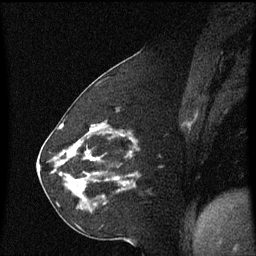
Breast MRI (dynamic contrast-enhanced), one sagittal slice; slice 23 of 60 in the series (ordered by position); dynamic contrast-enhanced series, image 2 of 3 at this slice position (ordered by acquisition); 1.5 T; TE 4.2 ms, TR 8.4 ms; 2.2 mm slice thickness; 256 × 256 image matrix, field of view 200 × 200 mm. Patient: female, 60 years. Case-level facts recorded for this patient, not image findings: setting: breast cancer imaged before/during neoadjuvant chemotherapy; receptor status: triple-negative.
Structures marked on this image (semi-automatic segmentation, software-assisted and operator-edited):
- analysis volume of interest (the breast-tissue region the enhancement analysis was run in; not a lesion): bounding box <68,142,137,213> (left, top, right, bottom; pixels)
- tumour enhancement mask (voxels above the 70 % enhancement threshold inside the analysis volume of interest): <71,152,129,191>